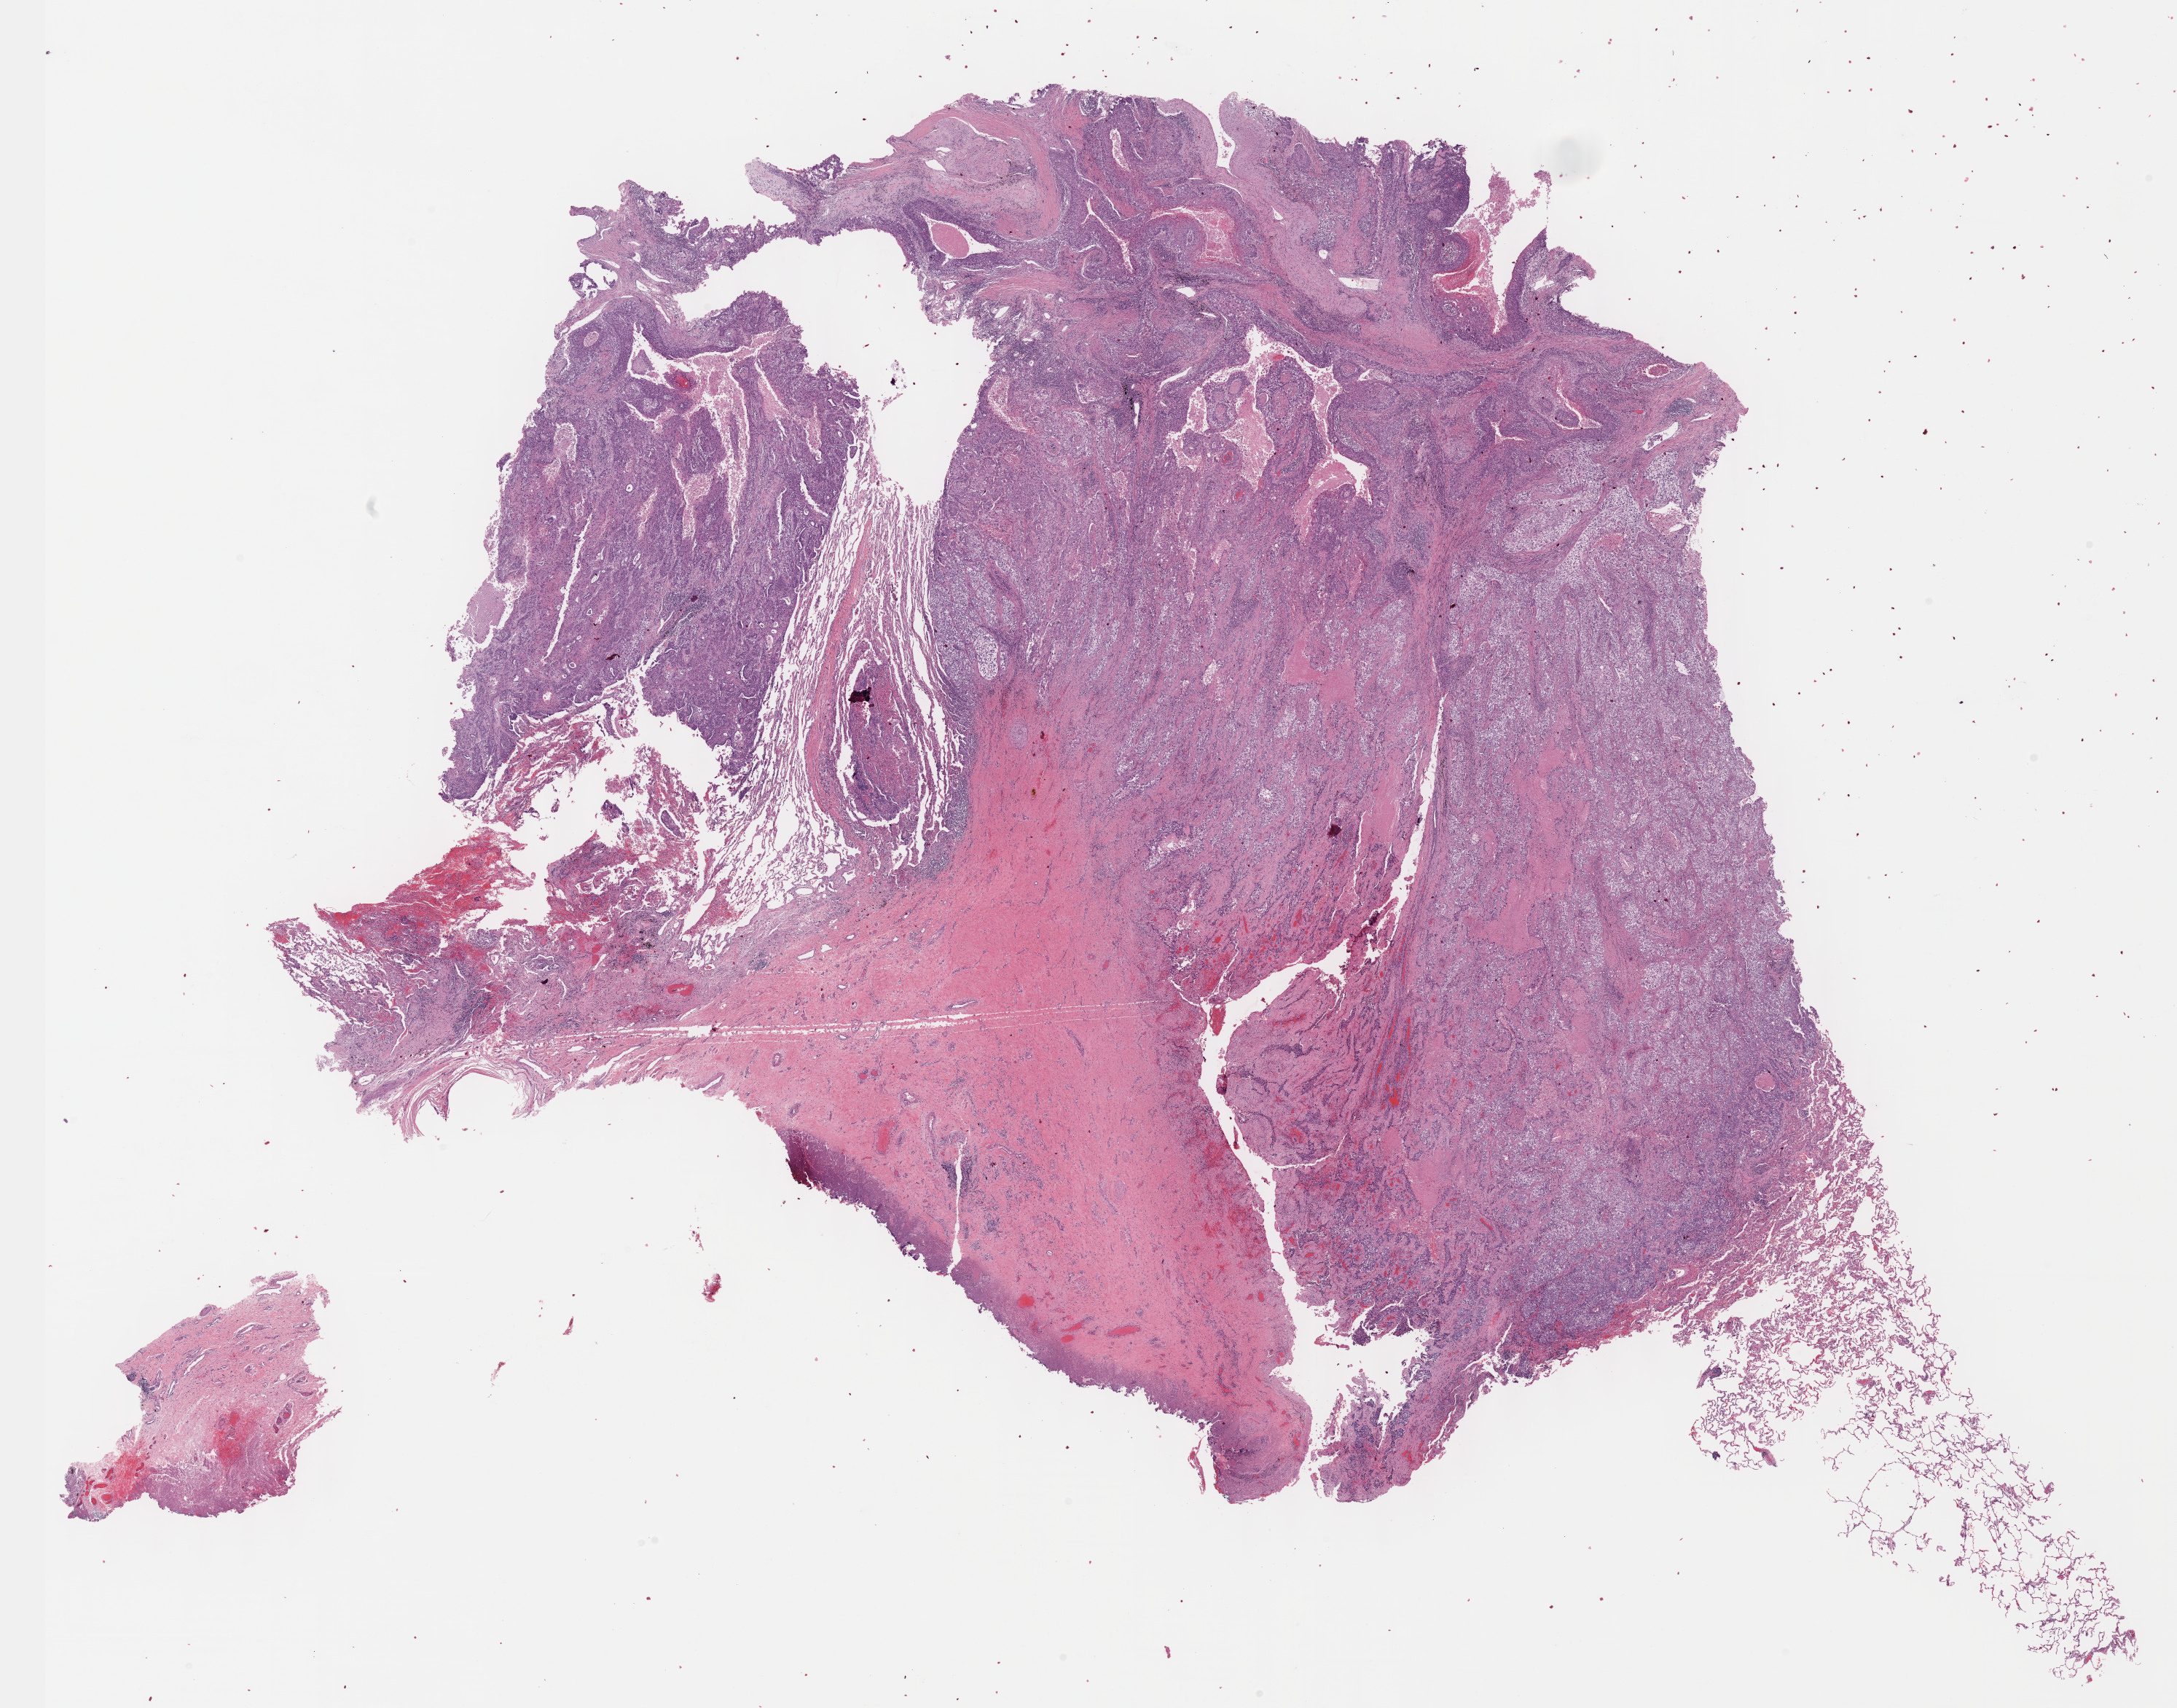
H&E whole-slide image — low-resolution overview of the scanned area, about 24.1 x 18.9 mm (from a 40x scan); formalin-fixed paraffin-embedded (FFPE) diagnostic section; primary tumour sample from the lung. Male, age 76 years at initial diagnosis.
• AJCC pathologic stage: IIIB
• histologic diagnosis: Squamous cell carcinoma, NOS